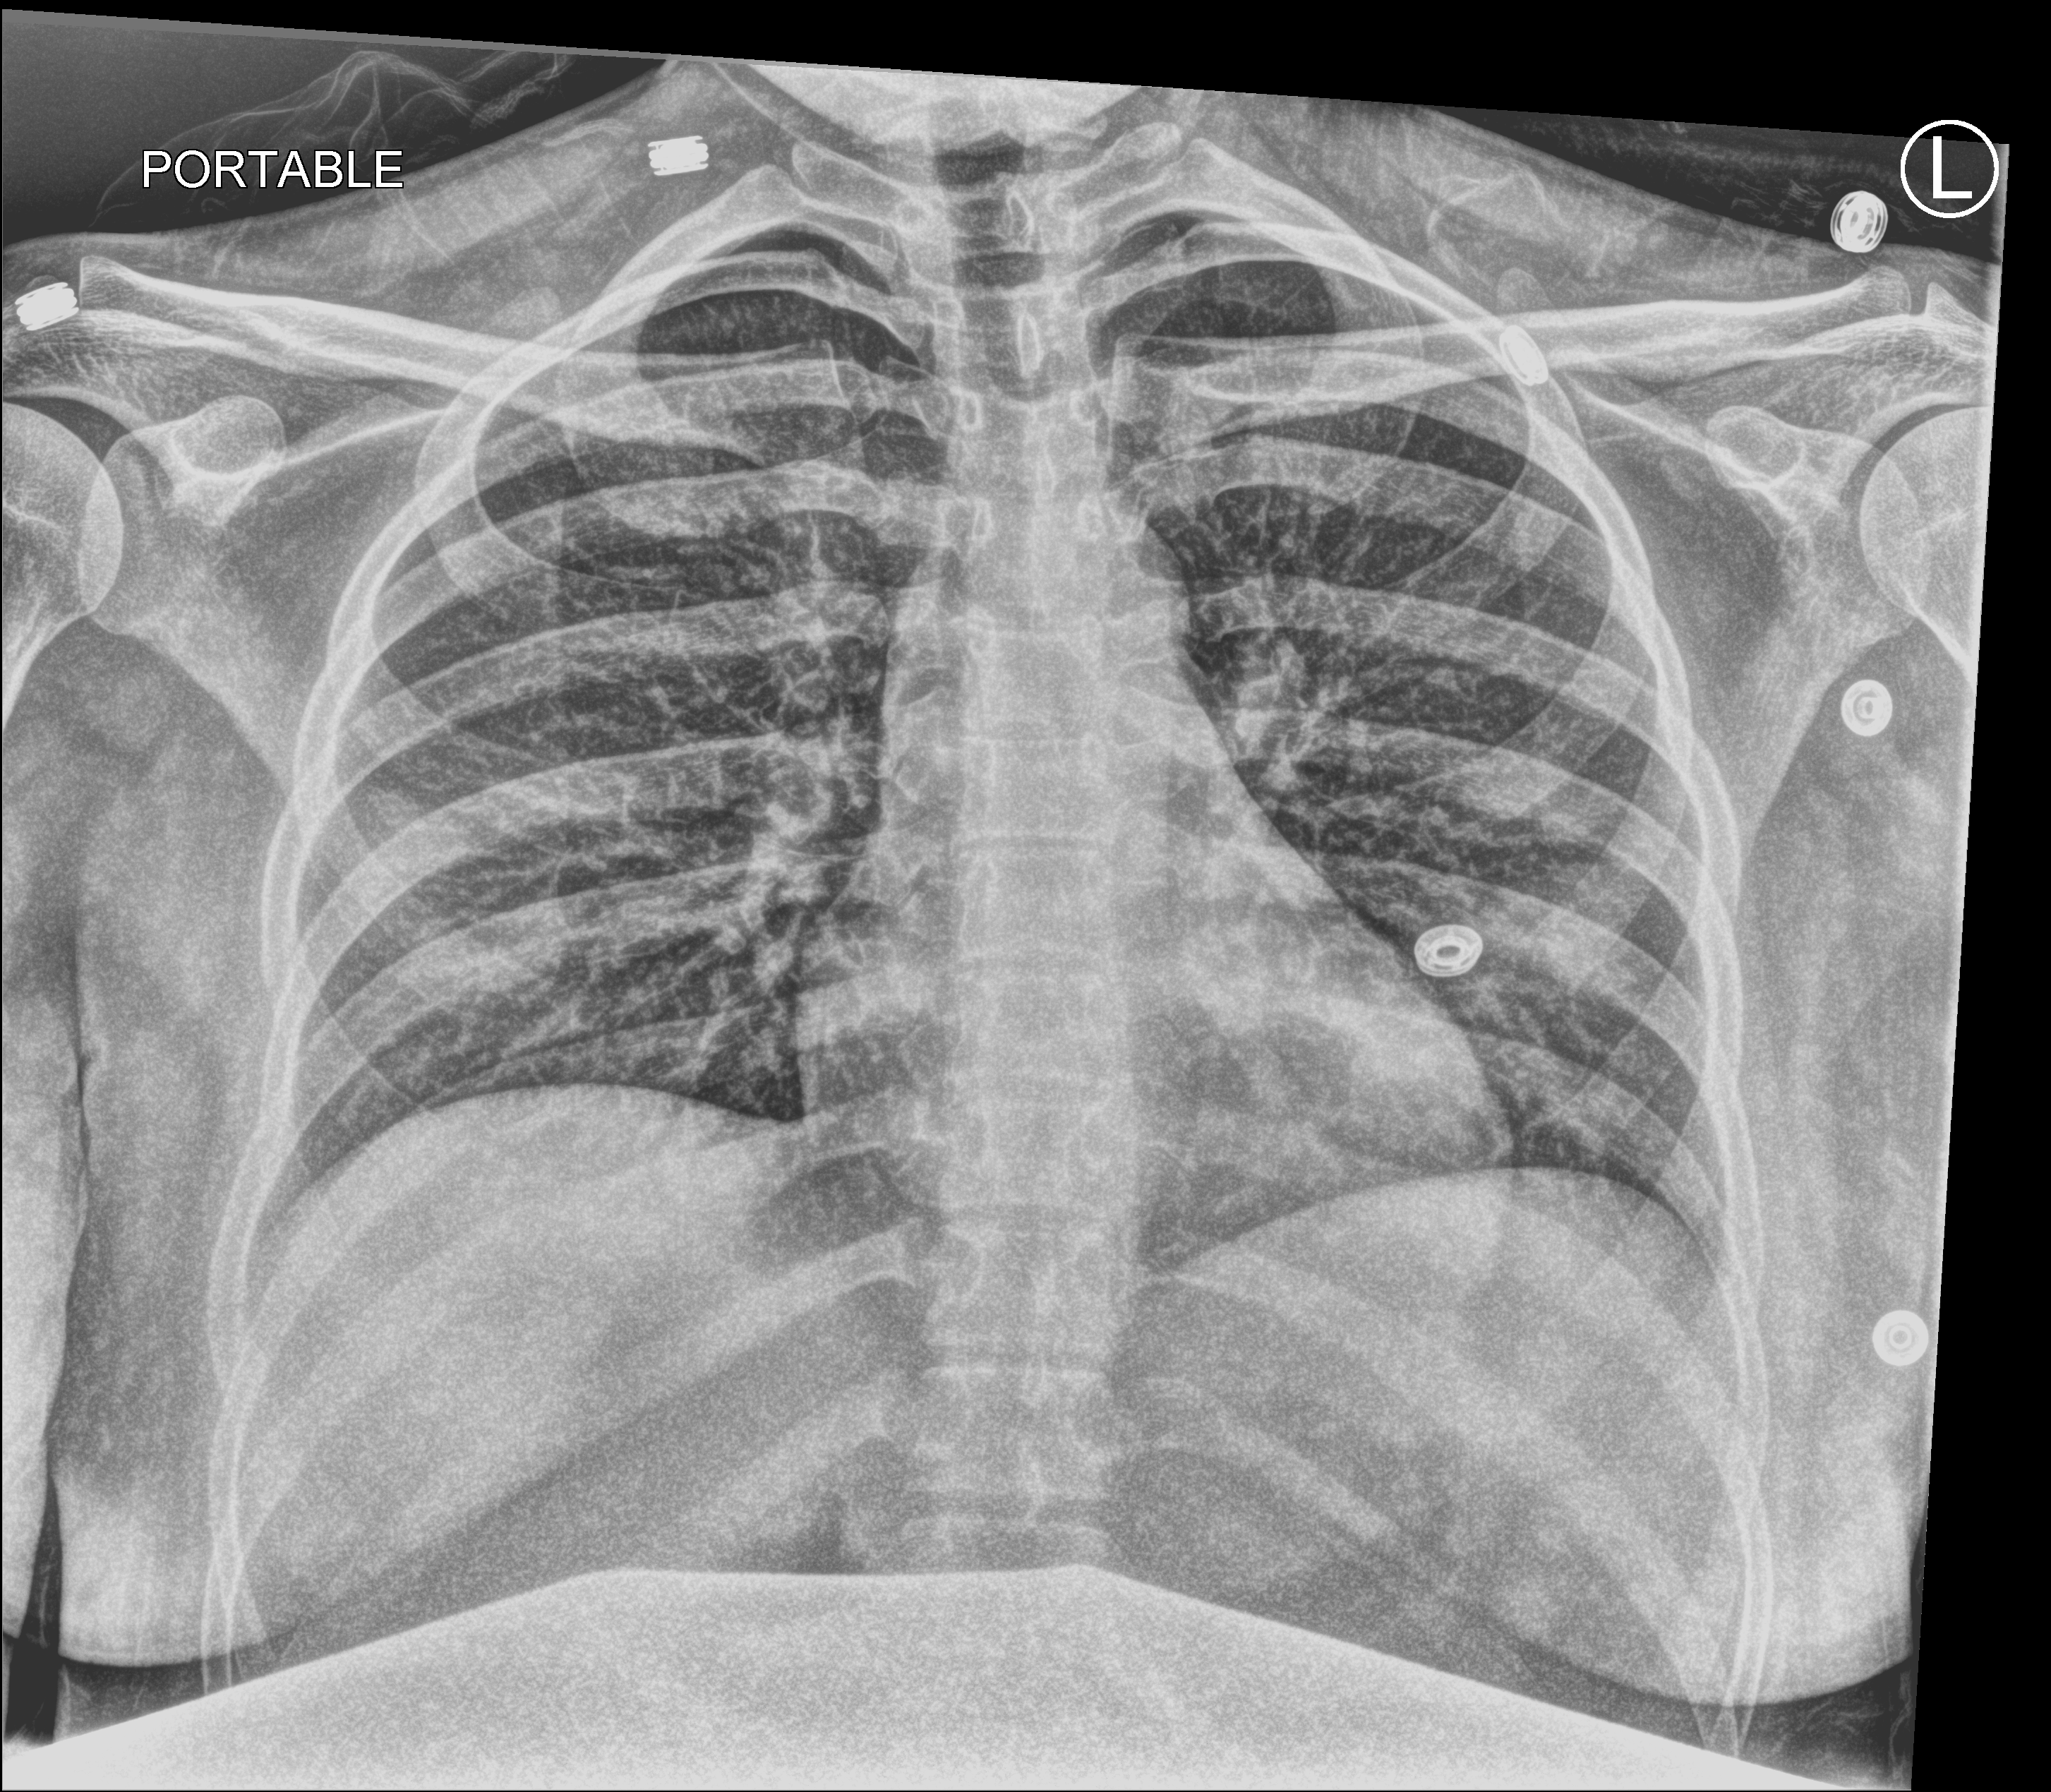
Portable chest radiograph; anteroposterior (AP) projection. Female patient hospitalised with COVID-19, age 18–59 years.
Hospital-stay facts (about this admission, not read from this image; timing relative to this image not recorded): mechanically ventilated during this hospital stay: no; admitted to intensive care during this hospital stay: no.